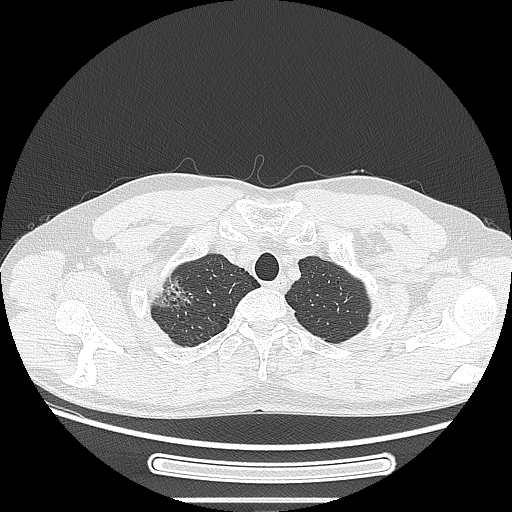
Chest CT, one axial slice; position 234 of 269 along the scan axis; reconstruction kernel LUNG; 120 kVp; lung window (W 1500 / L -600 HU); 1.25 mm slice thickness; 512 × 512 image matrix, field of view 382 × 382 mm. Male patient, age 53 years. From the clinical record (not read from this slice): clinical TNM (as recorded): T1c N0 M0.
Outlined on this slice (rectangle marked by the reading radiologist):
- lung tumour (recorded histology: adenocarcinoma): bounding box (x1, y1, x2, y2) in pixels: (142, 272, 202, 326)